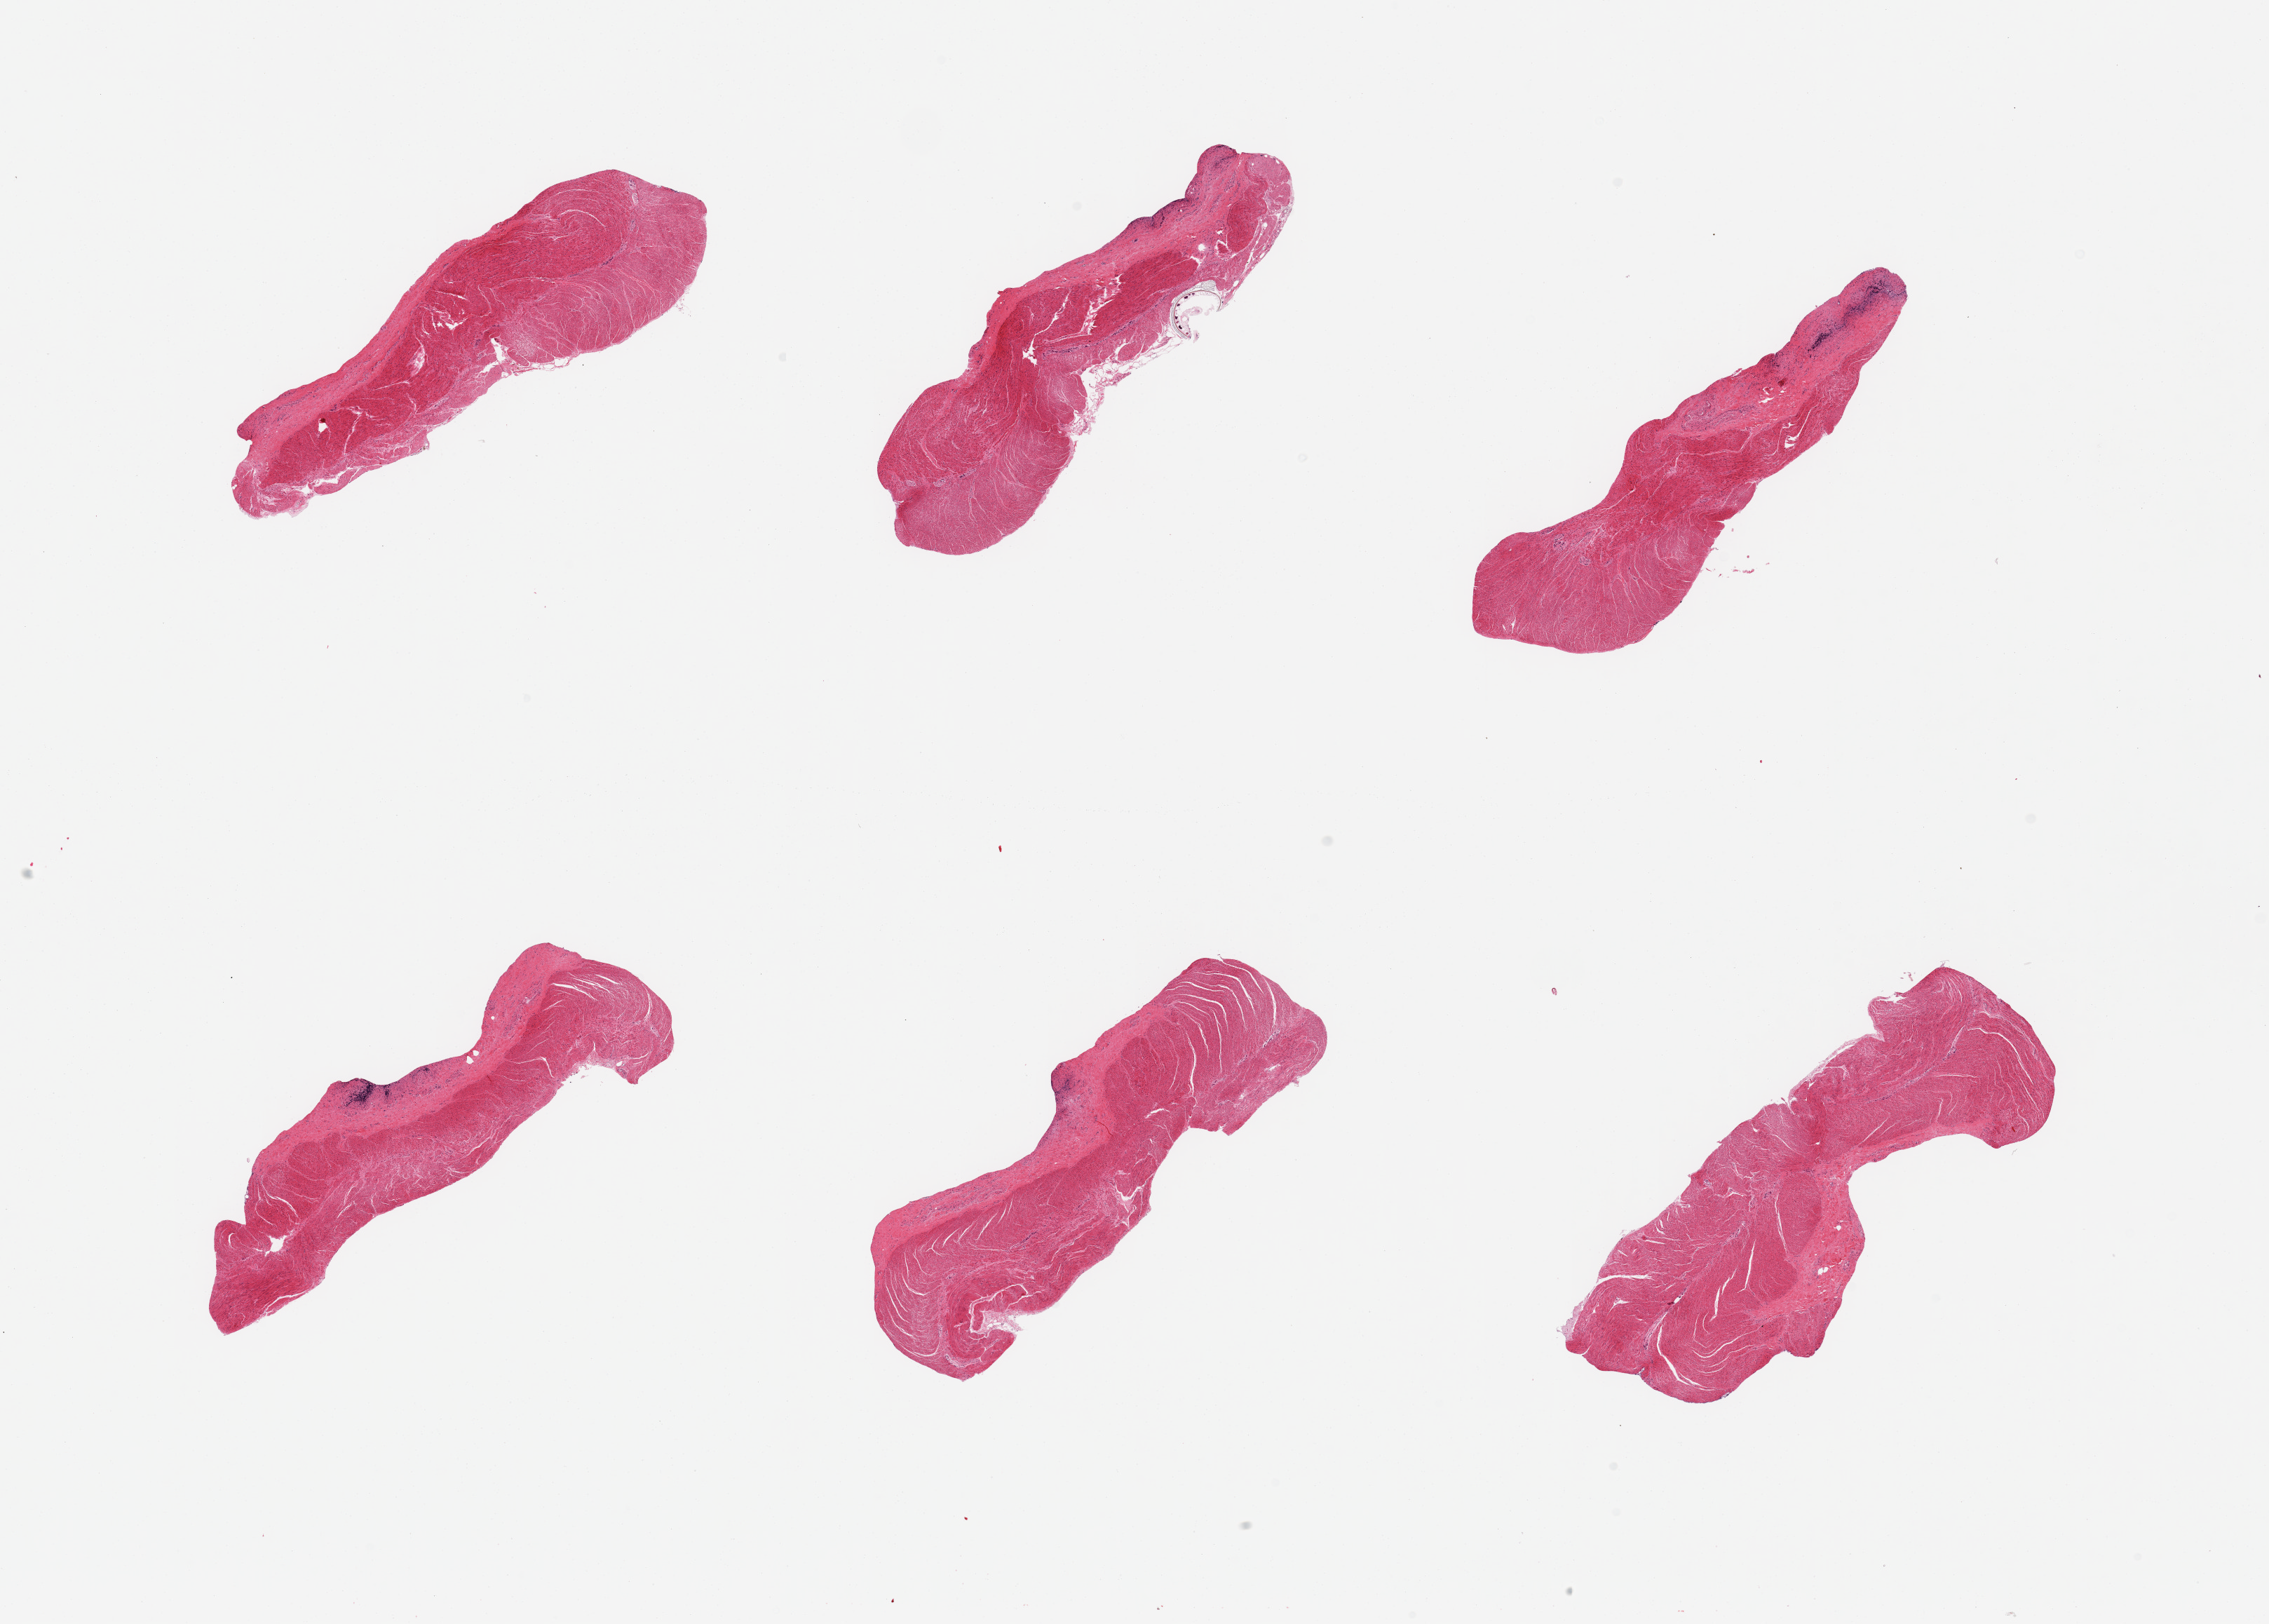
Digitized H&E-stained section, low-resolution overview of the scanned area, about 25.6 x 18.3 mm; PAXgene-fixed paraffin-embedded (PFPE) section; section of sigmoid colon (target tissue); tissue donor sample. Donor: male.
Pathologist's review note for this sample: 6 pieces; predominantly well trimmed.